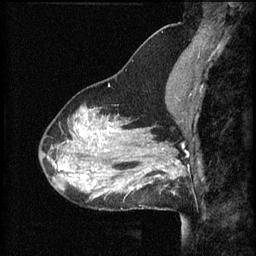
Breast MRI (dynamic contrast-enhanced), one sagittal slice; position 22 of 60 along the scan axis; 3 images stored at this slice position (order not interpretable as contrast timing); 1.5 T; TE 4.2 ms, TR 8.2 ms; 2 mm slice thickness; 256 × 256 image matrix, field of view 200 × 200 mm. Female patient, age 37 years.
Annotated regions visible in this slice (semi-automatic segmentation, software-assisted and operator-edited):
- analysis volume of interest (the breast-tissue region the enhancement analysis was run in; not a lesion): bounding box [x1, y1, x2, y2] px = [148, 140, 195, 195]
- tumour enhancement mask (voxels above the 70 % enhancement threshold inside the analysis volume of interest): [148, 160, 183, 183]